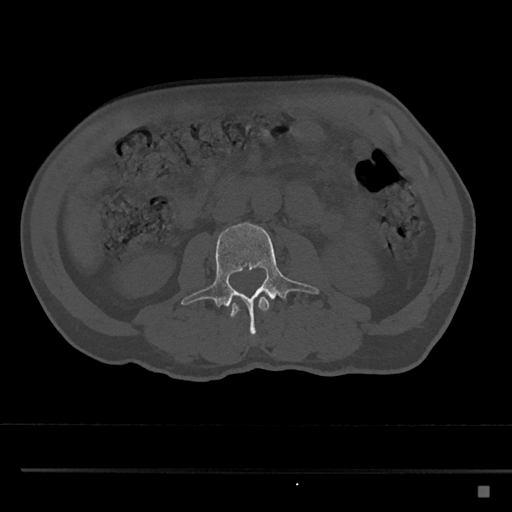
CT including the spine, one axial slice; slice 706 of 797 in the series (ordered by position); reconstruction kernel Br40s/3; 120 kVp; bone window (W 1800 / L 400 HU); 0.5 mm slice thickness; 512 × 512 image matrix, field of view 391 × 391 mm. Patient: male, 59 years. From the clinical record (not read from this slice): primary cancer: prostate.
Annotated regions visible in this slice (semi-automatic segmentation, software-assisted and operator-edited):
- L2 vertebra: bounding box <228,297,270,317> (left, top, right, bottom; pixels)
- L3 vertebra: <181,222,320,337>